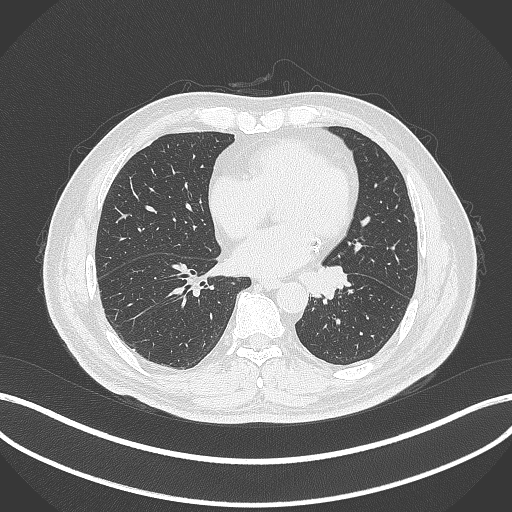
Chest CT, one axial slice; slice 112 of 312 in the series (ordered by position); reconstruction kernel B70f; lung window (W 1500 / L -600 HU); 1 mm slice thickness; 512 × 512 image matrix, field of view 400 × 400 mm. Male patient, age 71 years. From the clinical record (not read from this slice): clinical TNM (as recorded): T1b N0 M0.
Annotated regions visible in this slice (rectangle marked by the reading radiologist):
- lung tumour (recorded histology: squamous cell carcinoma): bounding box (x1, y1, x2, y2) in pixels: (297, 265, 353, 300)